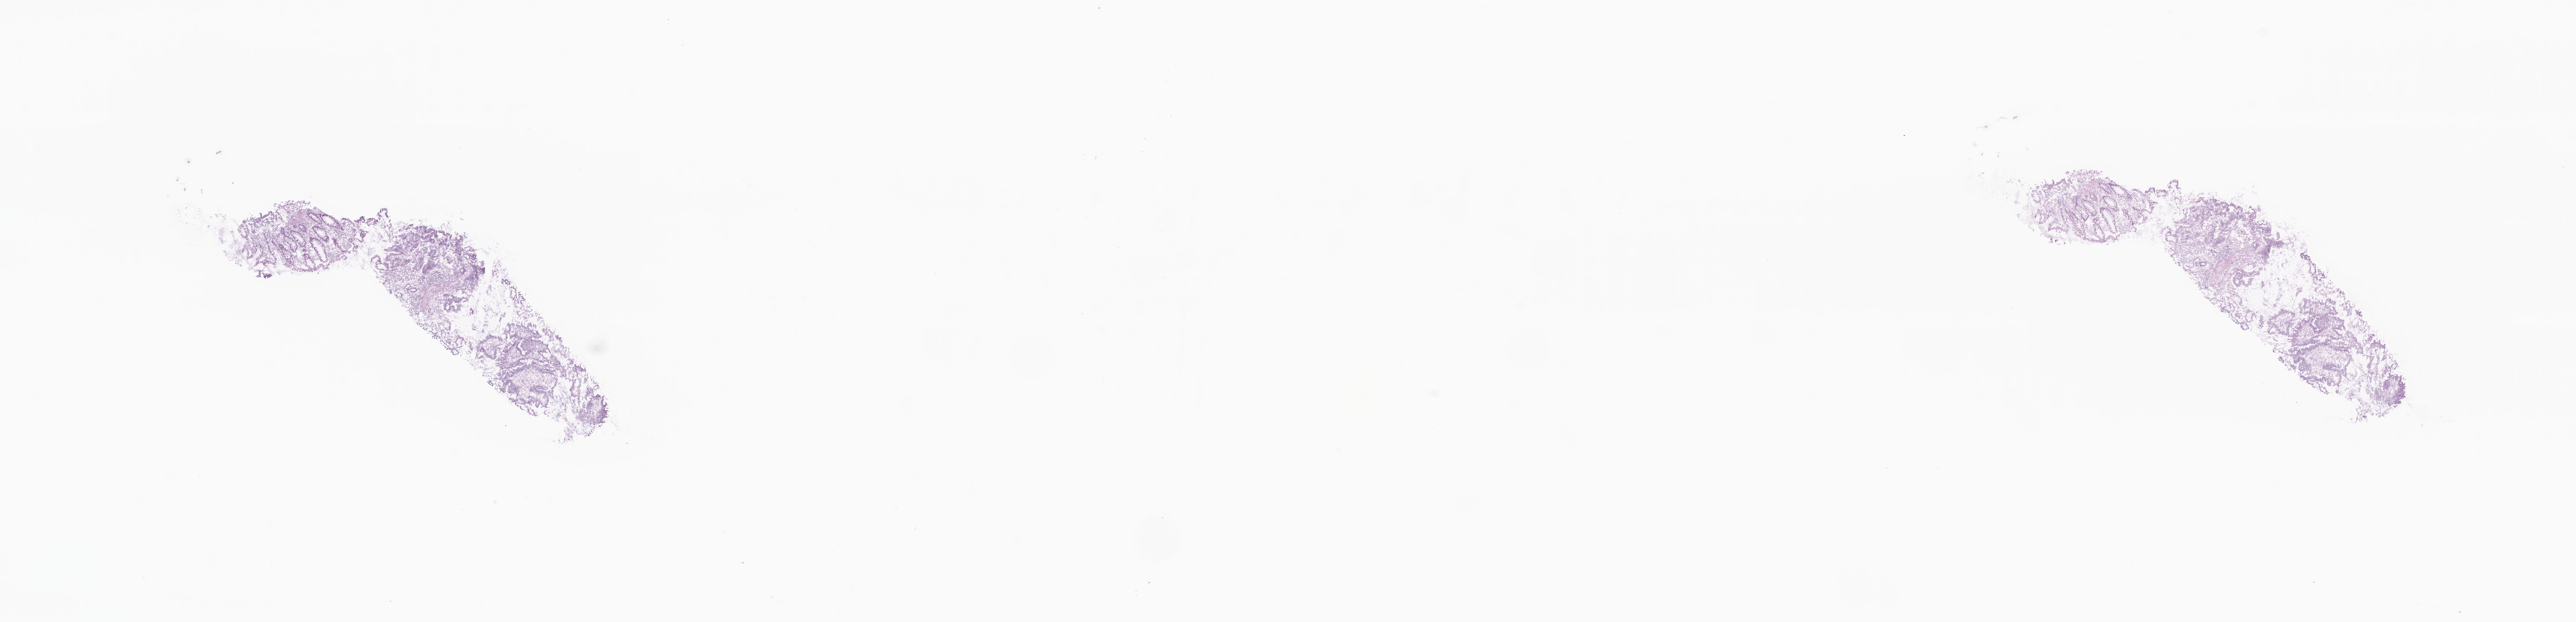
Hematoxylin and eosin (H&E) whole-slide image, a low-resolution overview of the entire scanned area, about 27.6 x 6.7 mm. Frozen section. Specimen: primary tumor. Site: descending colon. Male patient; age at initial diagnosis 65 years. Pathologist review of this section (percent, as recorded): tumor cells 50%, tumor nuclei 70%, stromal cells 30%, necrosis 0%, normal cells 20%. Inflammatory infiltration, as recorded: lymphocyte infiltration 0%, monocyte infiltration 0%, neutrophil infiltration 0%.
* histologic diagnosis: Adenocarcinoma, NOS